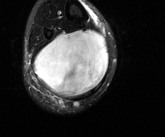
MRI of an extremity soft-tissue mass, one axial slice; slice 47 of 81 in the series (ordered by position); T2-weighted fat-saturated; MR volume resampled by the dataset authors to the PET/CT grid (not the native acquisition matrix); 165 × 137 image matrix, field of view 161 × 134 mm. Male patient. Case-level facts recorded for this patient, not image findings: histological type: liposarcoma - round cell; grade: high; site of the primary tumour: right calf.
Annotated regions visible in this slice (expert contour drawn on MRI and transferred to this co-registered scan by the dataset authors):
- gross tumour volume (mass): box from (x=34, y=30) to (x=109, y=97) px